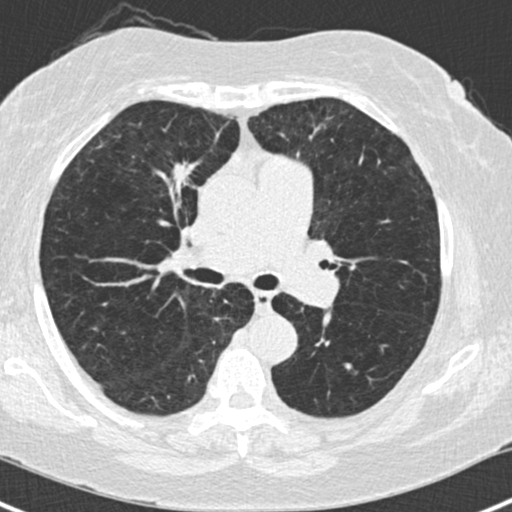
Low-dose screening chest CT, one axial slice; position 91 of 168 along the scan axis; lung window (W 1500 / L -600 HU); 512 × 512 image matrix, field of view 303 × 303 mm.
Annotated regions visible in this slice (manually delineated by an expert):
- lesion 1 (tumor, upper lobe of right lung): bounding box [x1, y1, x2, y2] px = [173, 162, 199, 189]